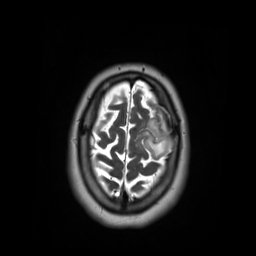
Brain MRI from a brain-tumour surgery series, one axial slice; position 48 of 59 along the scan axis; 256 × 256 image matrix, field of view 250 × 250 mm. Case-level facts recorded for this patient, not image findings: histopathology: Oligodendroglioma; WHO grade: 2; IDH mutation: yes.
Annotated regions visible in this slice (manually delineated by an expert):
- tumour: bounding box [x1, y1, x2, y2] px = [139, 120, 180, 158]